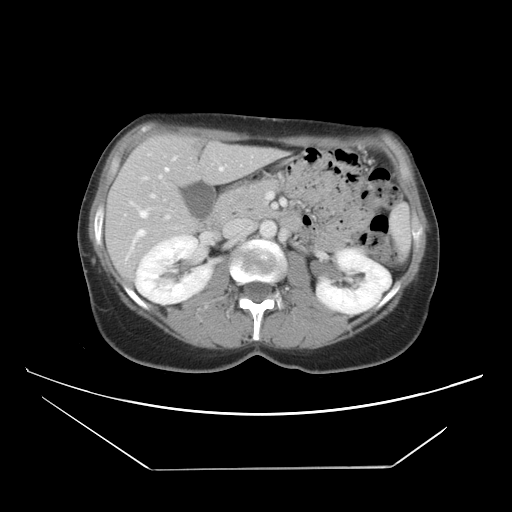
Contrast-enhanced abdominal CT, one axial slice. Slice 22 of 42 in the series (ordered by position). 120 kVp. Soft-tissue window (W 400 / L 40 HU). 5 mm slice thickness. 512 × 512 image matrix. Female patient, age 52 years. Case-level facts recorded for this patient, not image findings: diagnosis: colorectal cancer liver metastases, imaged before liver resection; multiple liver metastases: yes; largest metastasis: 5.5 cm.
Annotated regions visible in this slice (expert manual segmentation):
- hepatic veins: box from (x=129, y=152) to (x=224, y=244) px
- liver: (x=106, y=135)–(x=281, y=276)
- planned liver remnant (the part of the liver to remain after resection): (x=114, y=135)–(x=217, y=209)
- portal vein (with intrahepatic branches): (x=151, y=155)–(x=270, y=219)